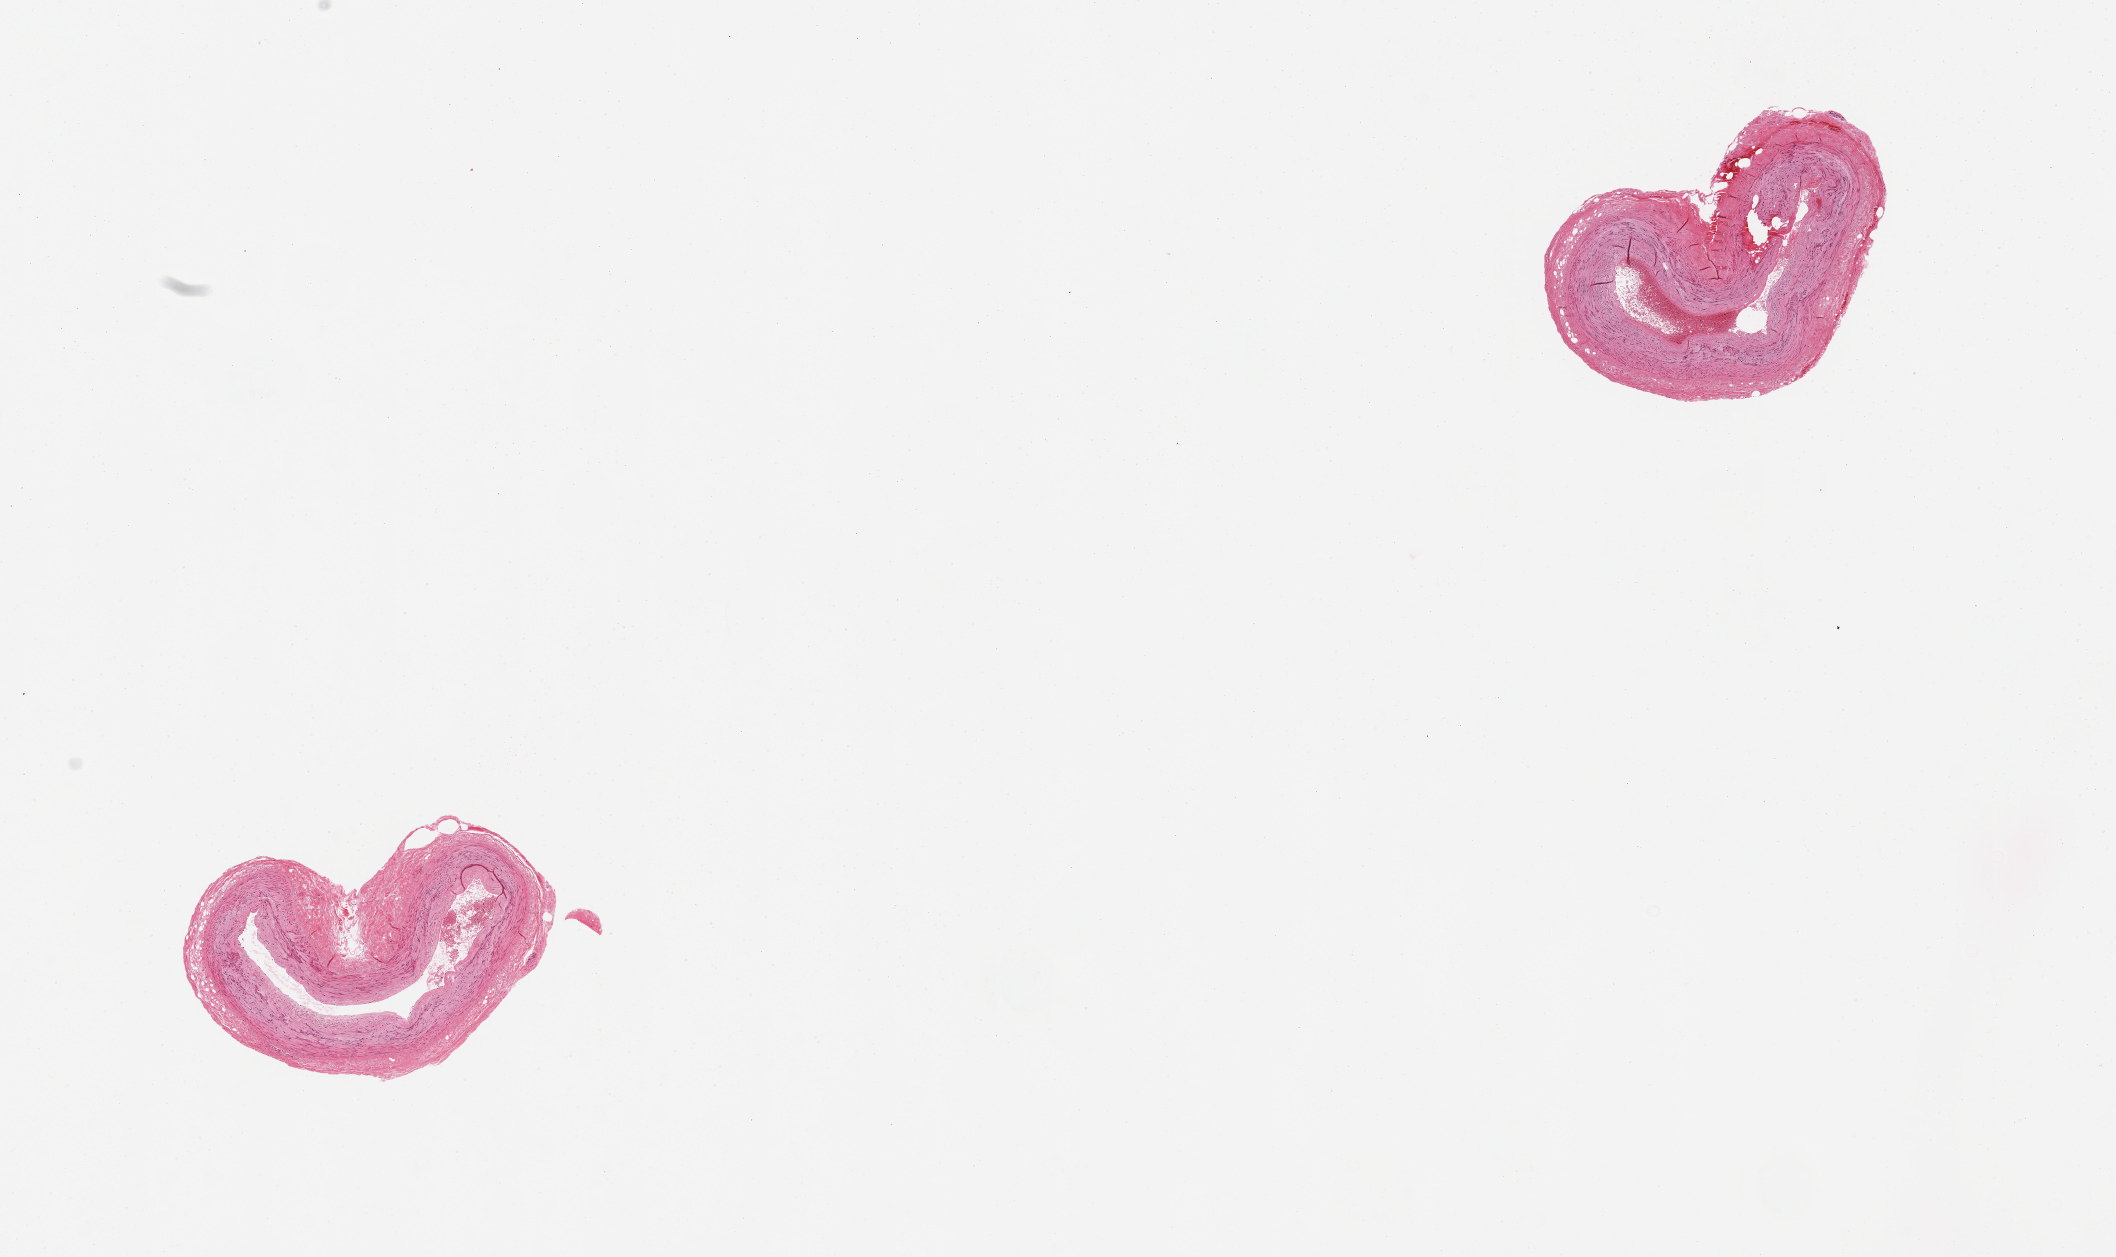
Whole-slide image, haematoxylin and eosin stain — a low-resolution overview of the entire scanned area, about 16.7 x 9.9 mm (acquisition: 20x scan). PAXgene-fixed paraffin-embedded (PFPE) section. Target tissue: tibial artery. Tissue donor sample. Male donor.
Pathologist's review note for this sample: 2 pieces, well trimmed.